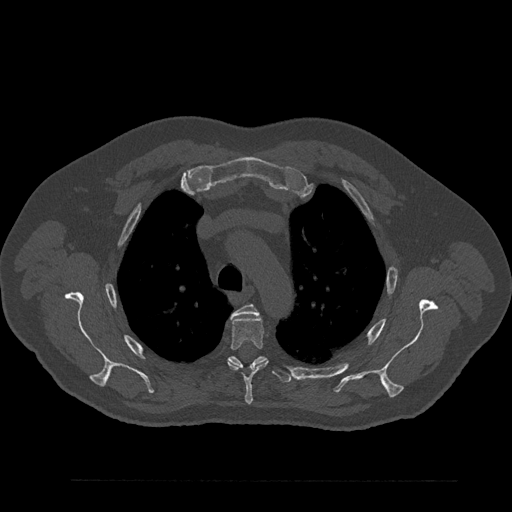
CT including the spine, one axial slice; position 635 of 797 along the scan axis; bone window (W 1800 / L 400 HU); 512 × 512 image matrix, field of view 430 × 430 mm. Male patient, age 61 years. Case-level facts recorded for this patient, not image findings: primary cancer: prostate.
Annotated regions visible in this slice (semi-automatically segmented with operator editing):
- T3 vertebra: bounding box [x1, y1, x2, y2] px = [230, 304, 258, 318]
- T4 vertebra: [227, 316, 268, 405]
- T5 vertebra: [207, 356, 291, 383]